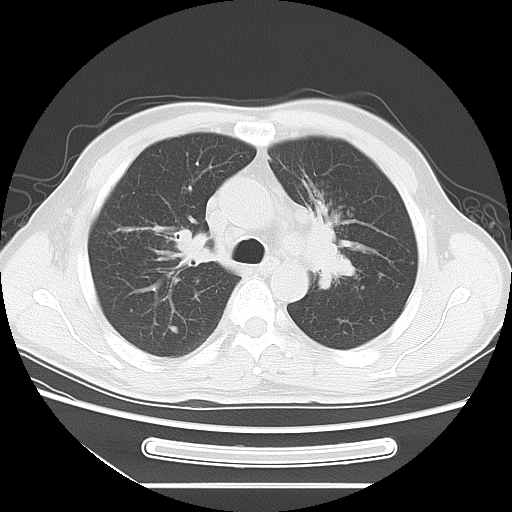
Chest CT, one axial slice; slice 49 of 71 in the series (ordered by position); reconstruction kernel LUNG; 120 kVp; lung window (W 1500 / L -600 HU); 5 mm slice thickness; 512 × 512 image matrix. Patient: male, 51 years. From the clinical record (not read from this slice): clinical TNM (as recorded): T1c N3 M0.
Outlined on this slice (bounding box drawn by a radiologist):
- lung tumour (recorded histology: adenocarcinoma): box from (x=300, y=189) to (x=363, y=288) px